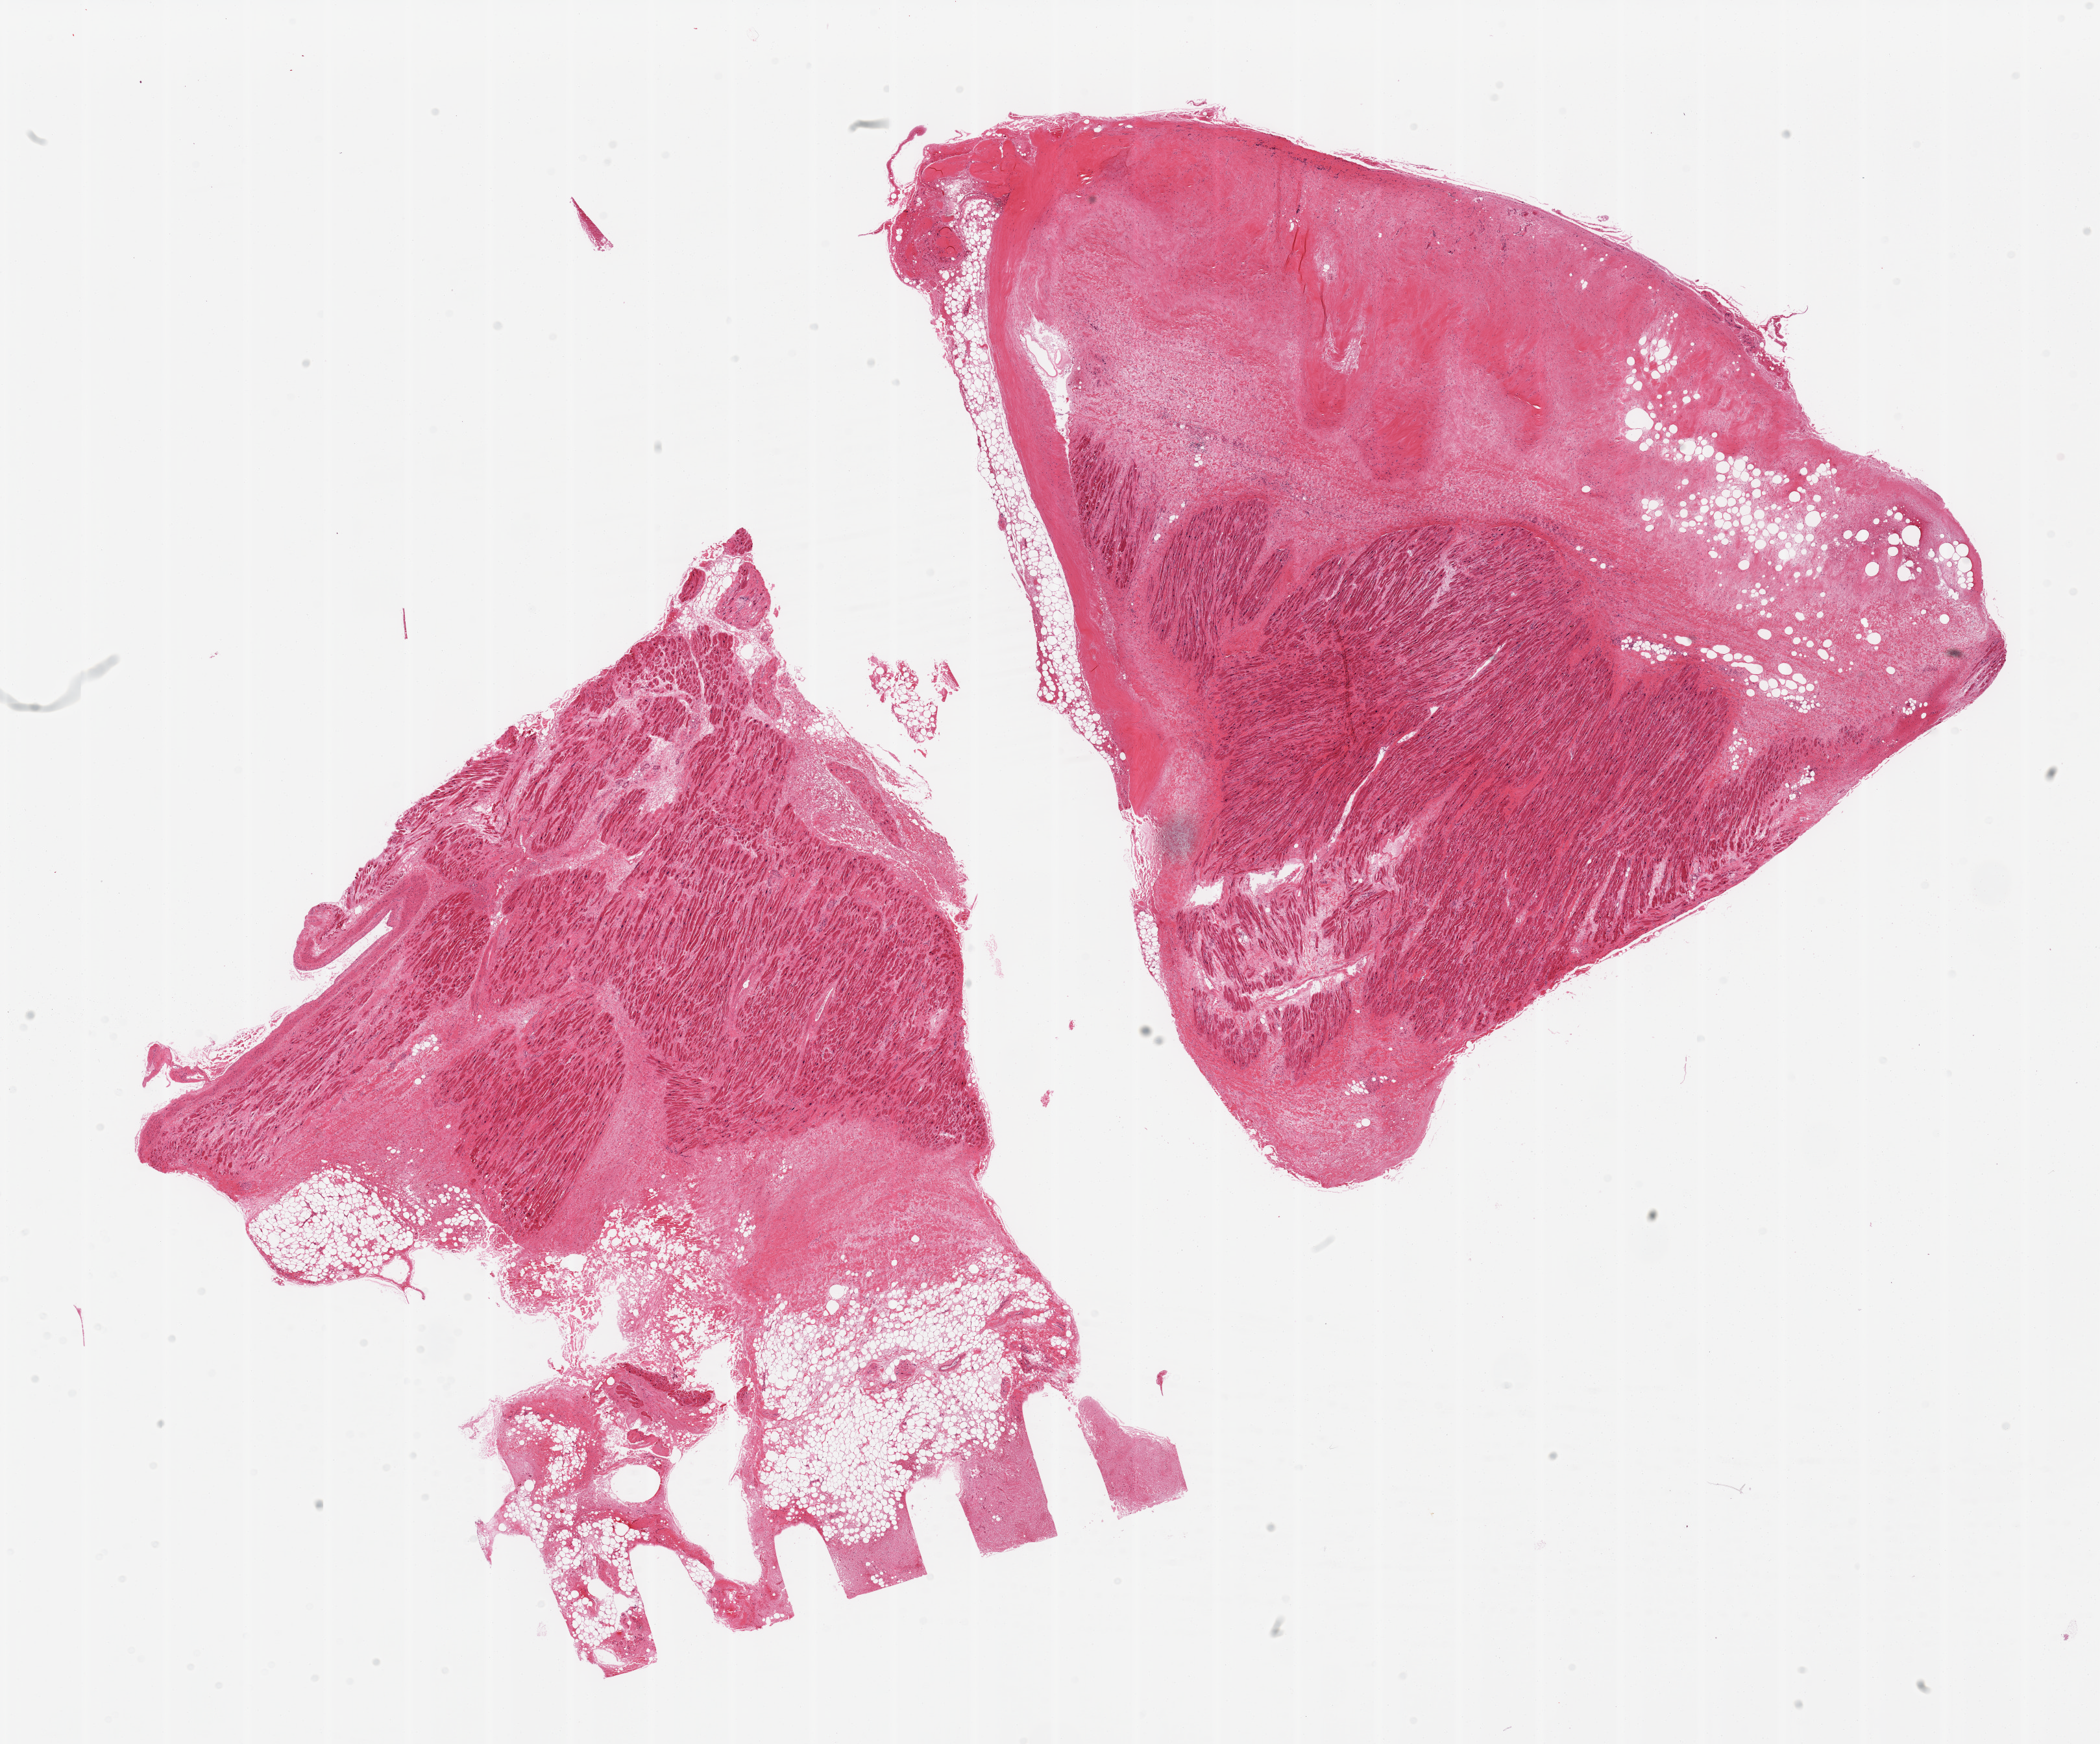
H&E whole-slide image — low-resolution overview of the scanned area, about 25.6 x 21.3 mm. PAXgene-fixed paraffin-embedded (PFPE) section. Sampled site (target tissue): auricular appendage. Donor tissue sample. Donor: male.
Reviewer comment on this tissue sample: 2 pieces, aliquots partially acutely infarcted.